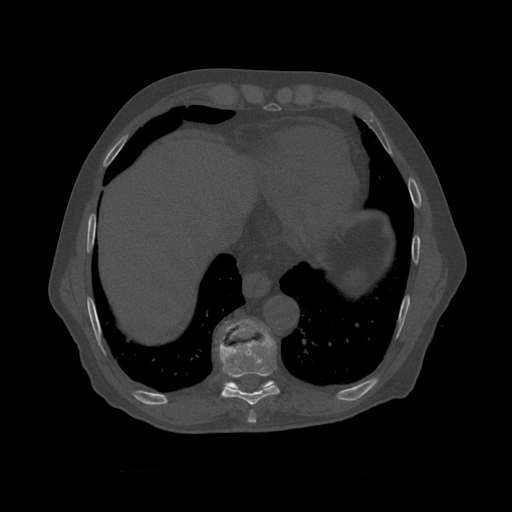
CT including the spine, one axial slice. Position 441 of 450 along the scan axis. 120 kVp. Bone window (W 1800 / L 400 HU). 1.25 mm slice thickness. 512 × 512 image matrix, field of view 405 × 405 mm. Patient age 75 years. From the clinical record (not read from this slice): primary cancer: prostate.
Annotated regions visible in this slice (semi-automatically segmented with operator editing):
- T8 vertebra: box from (x=218, y=323) to (x=280, y=407) px
- T9 vertebra: (x=224, y=319)–(x=275, y=390)